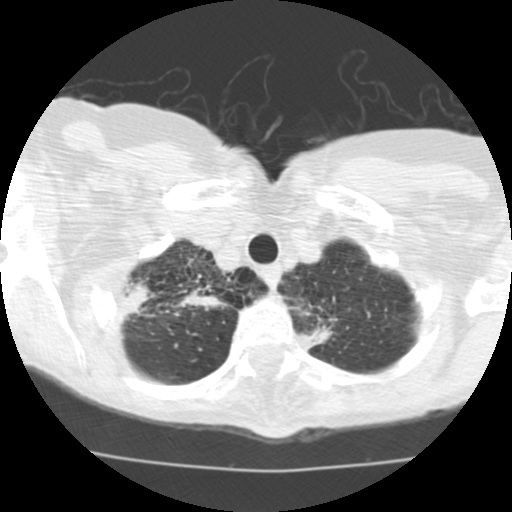
Low-dose screening chest CT, one axial slice; 120 kVp; lung window (W 1500 / L -600 HU); 2.5 mm slice thickness; 512 × 512 image matrix, field of view 280 × 280 mm.
Outlined on this slice (manually delineated by an expert):
- lesion 1 (tumor, upper lobe of right lung): bounding box [x1, y1, x2, y2] px = [124, 280, 155, 317]